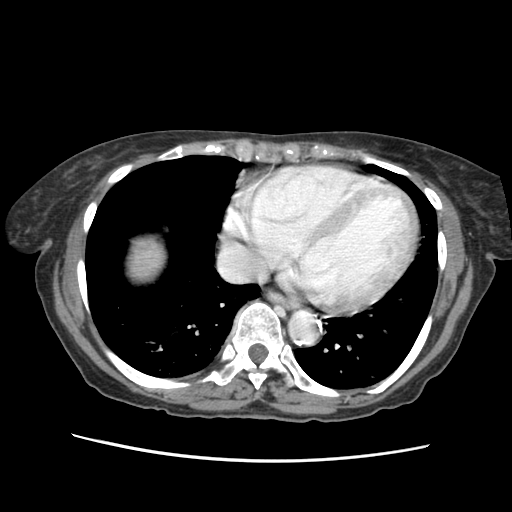
Contrast-enhanced abdominal CT (liver protocol), one axial slice; position 59 of 63 along the scan axis; reconstruction kernel STANDARD; 120 kVp; soft-tissue window (W 400 / L 40 HU); 2.5 mm slice thickness; 512 × 512 image matrix, field of view 340 × 340 mm. Case-level facts recorded for this patient, not image findings: diagnosis: hepatocellular carcinoma (patient treated with transarterial chemoembolisation; whether this scan precedes or follows treatment is not stated here); TNM stage (as recorded): Stage-I; Child-Pugh class: B.
Annotated regions visible in this slice (semi-automatically segmented with operator editing):
- liver parenchyma outside the tumour (the mass and vessels are separate outlines, so this box may not span the whole liver): box from (x=132, y=242) to (x=160, y=276) px